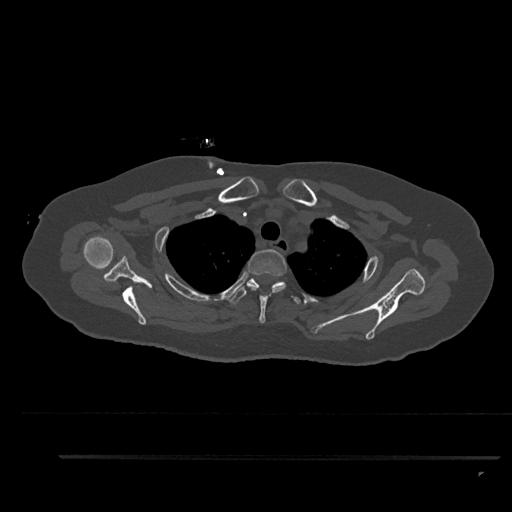
CT including the spine, one axial slice; position 705 of 797 along the scan axis; 120 kVp; bone window (W 1800 / L 400 HU); 0.5 mm slice thickness; 512 × 512 image matrix. Female patient, age 44 years. Case-level facts recorded for this patient, not image findings: primary cancer: renal.
Structures marked on this image (semi-automatically segmented with operator editing):
- T1 vertebra: bounding box <282,284,286,286> (left, top, right, bottom; pixels)
- T2 vertebra: <246,249,287,323>
- T3 vertebra: <229,278,301,305>